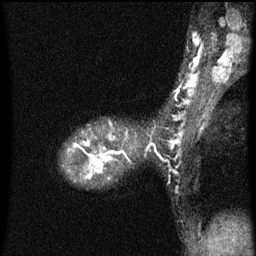
Breast MRI (dynamic contrast-enhanced), one sagittal slice. Slice 40 of 60 in the series (ordered by position). Dynamic contrast-enhanced series, image 2 of 3 at this slice position (ordered by acquisition). 1.5 T. TE 4.2 ms, TR 8 ms. 256 × 256 image matrix, field of view 180 × 180 mm. Patient: female, 36 years.
Structures marked on this image (semi-automatically segmented with operator editing):
- analysis volume of interest (the breast-tissue region the enhancement analysis was run in; not a lesion): bounding box <86,146,109,161> (left, top, right, bottom; pixels)
- tumour enhancement mask (voxels above the 70 % enhancement threshold inside the analysis volume of interest): <86,146,109,161>